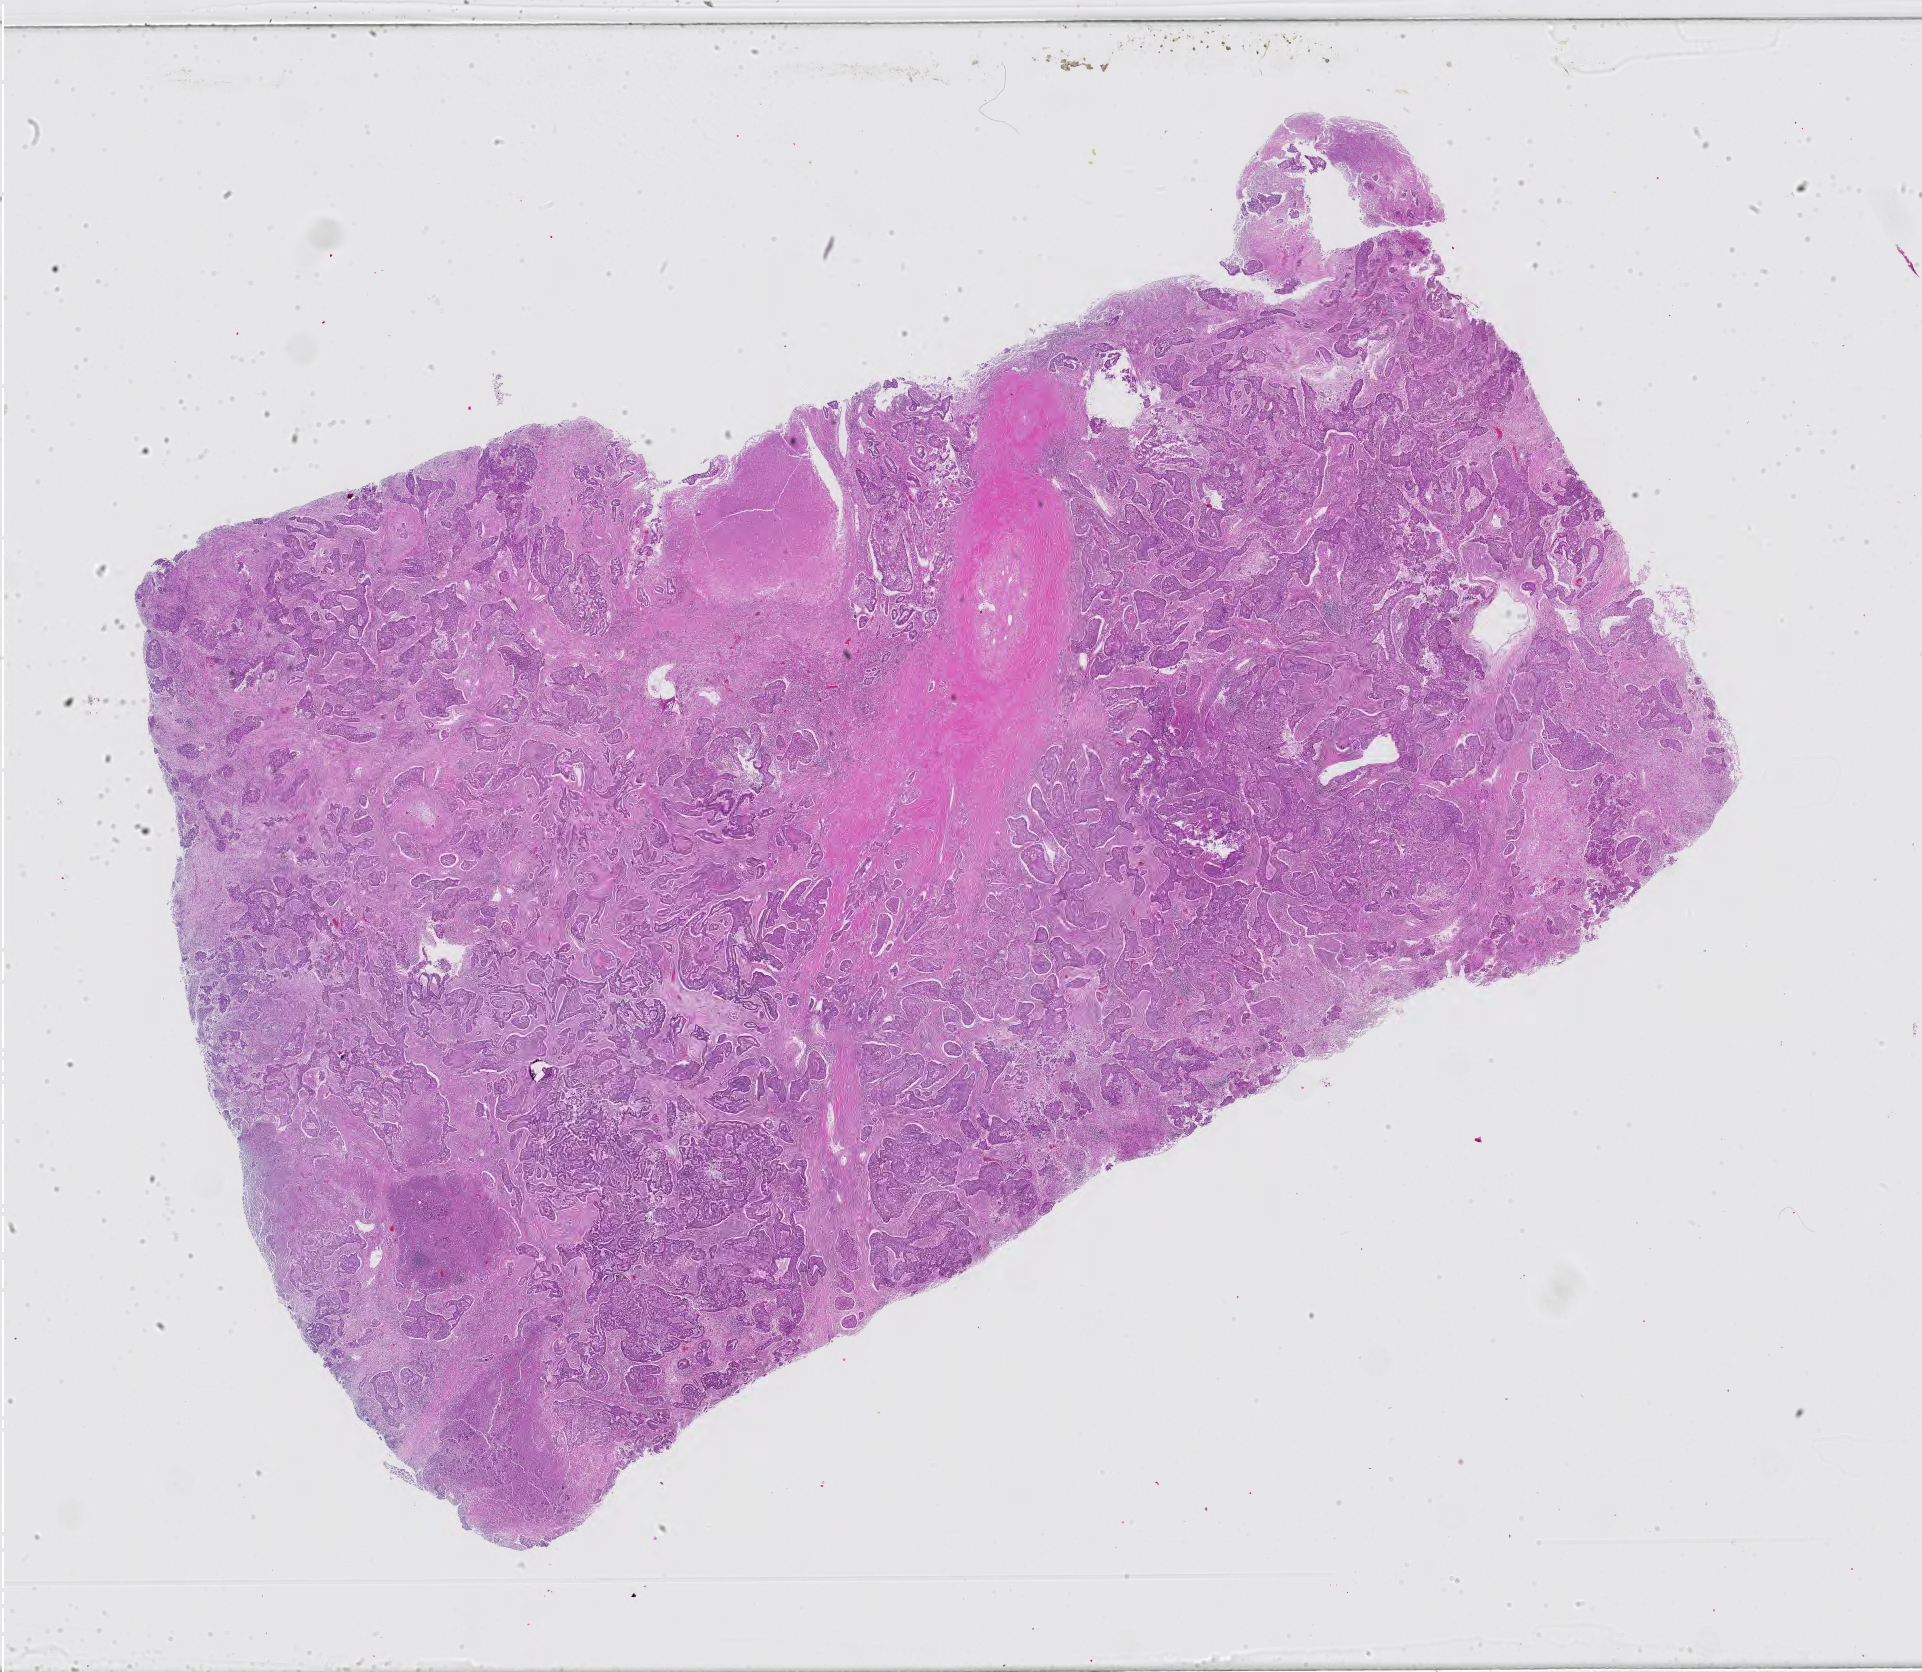
Whole-slide histology image, H&E-stained — whole scanned area (about 27.9 x 24.2 mm) shown as a low-resolution overview; formalin-fixed paraffin-embedded (FFPE) diagnostic section; sample: primary tumour, lung. Female patient; age at initial diagnosis 66 years.
Laterality: left. AJCC pathologic stage: IIIA (7th edition). Diagnosis: Acinar cell carcinoma (lower lobe, lung).